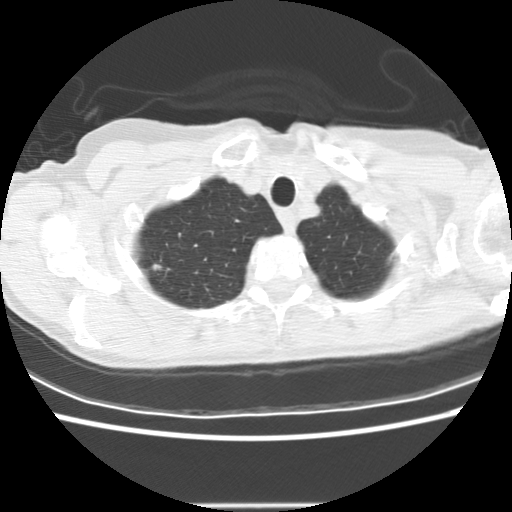
Low-dose screening chest CT, axial slice, second annual screen, lung window (W 1500 / L -600 HU), 2.5 mm slice thickness, 120 kVp, slice 15 of 166 in the series. Female participant, aged 58 years at enrolment.
Lesion marked by an expert reader, box from (x=137, y=252) to (x=175, y=286) px. The screening reader recorded 2 non-calcified nodules or masses ≥4 mm on this exam; which of them this box marks is not recorded. Official screen result: positive, change unspecified: nodule(s) >= 4 mm or enlarging nodule(s), mass(es), or other non-specific abnormalities suspicious for lung cancer. Later outcome: lung cancer diagnosed 434 days after this screen — bronchiolo-alveolar adenocarcinoma, NOS, right upper lobe, well differentiated (G1), stage IA (AJCC 6th edition), 8 mm at pathology.